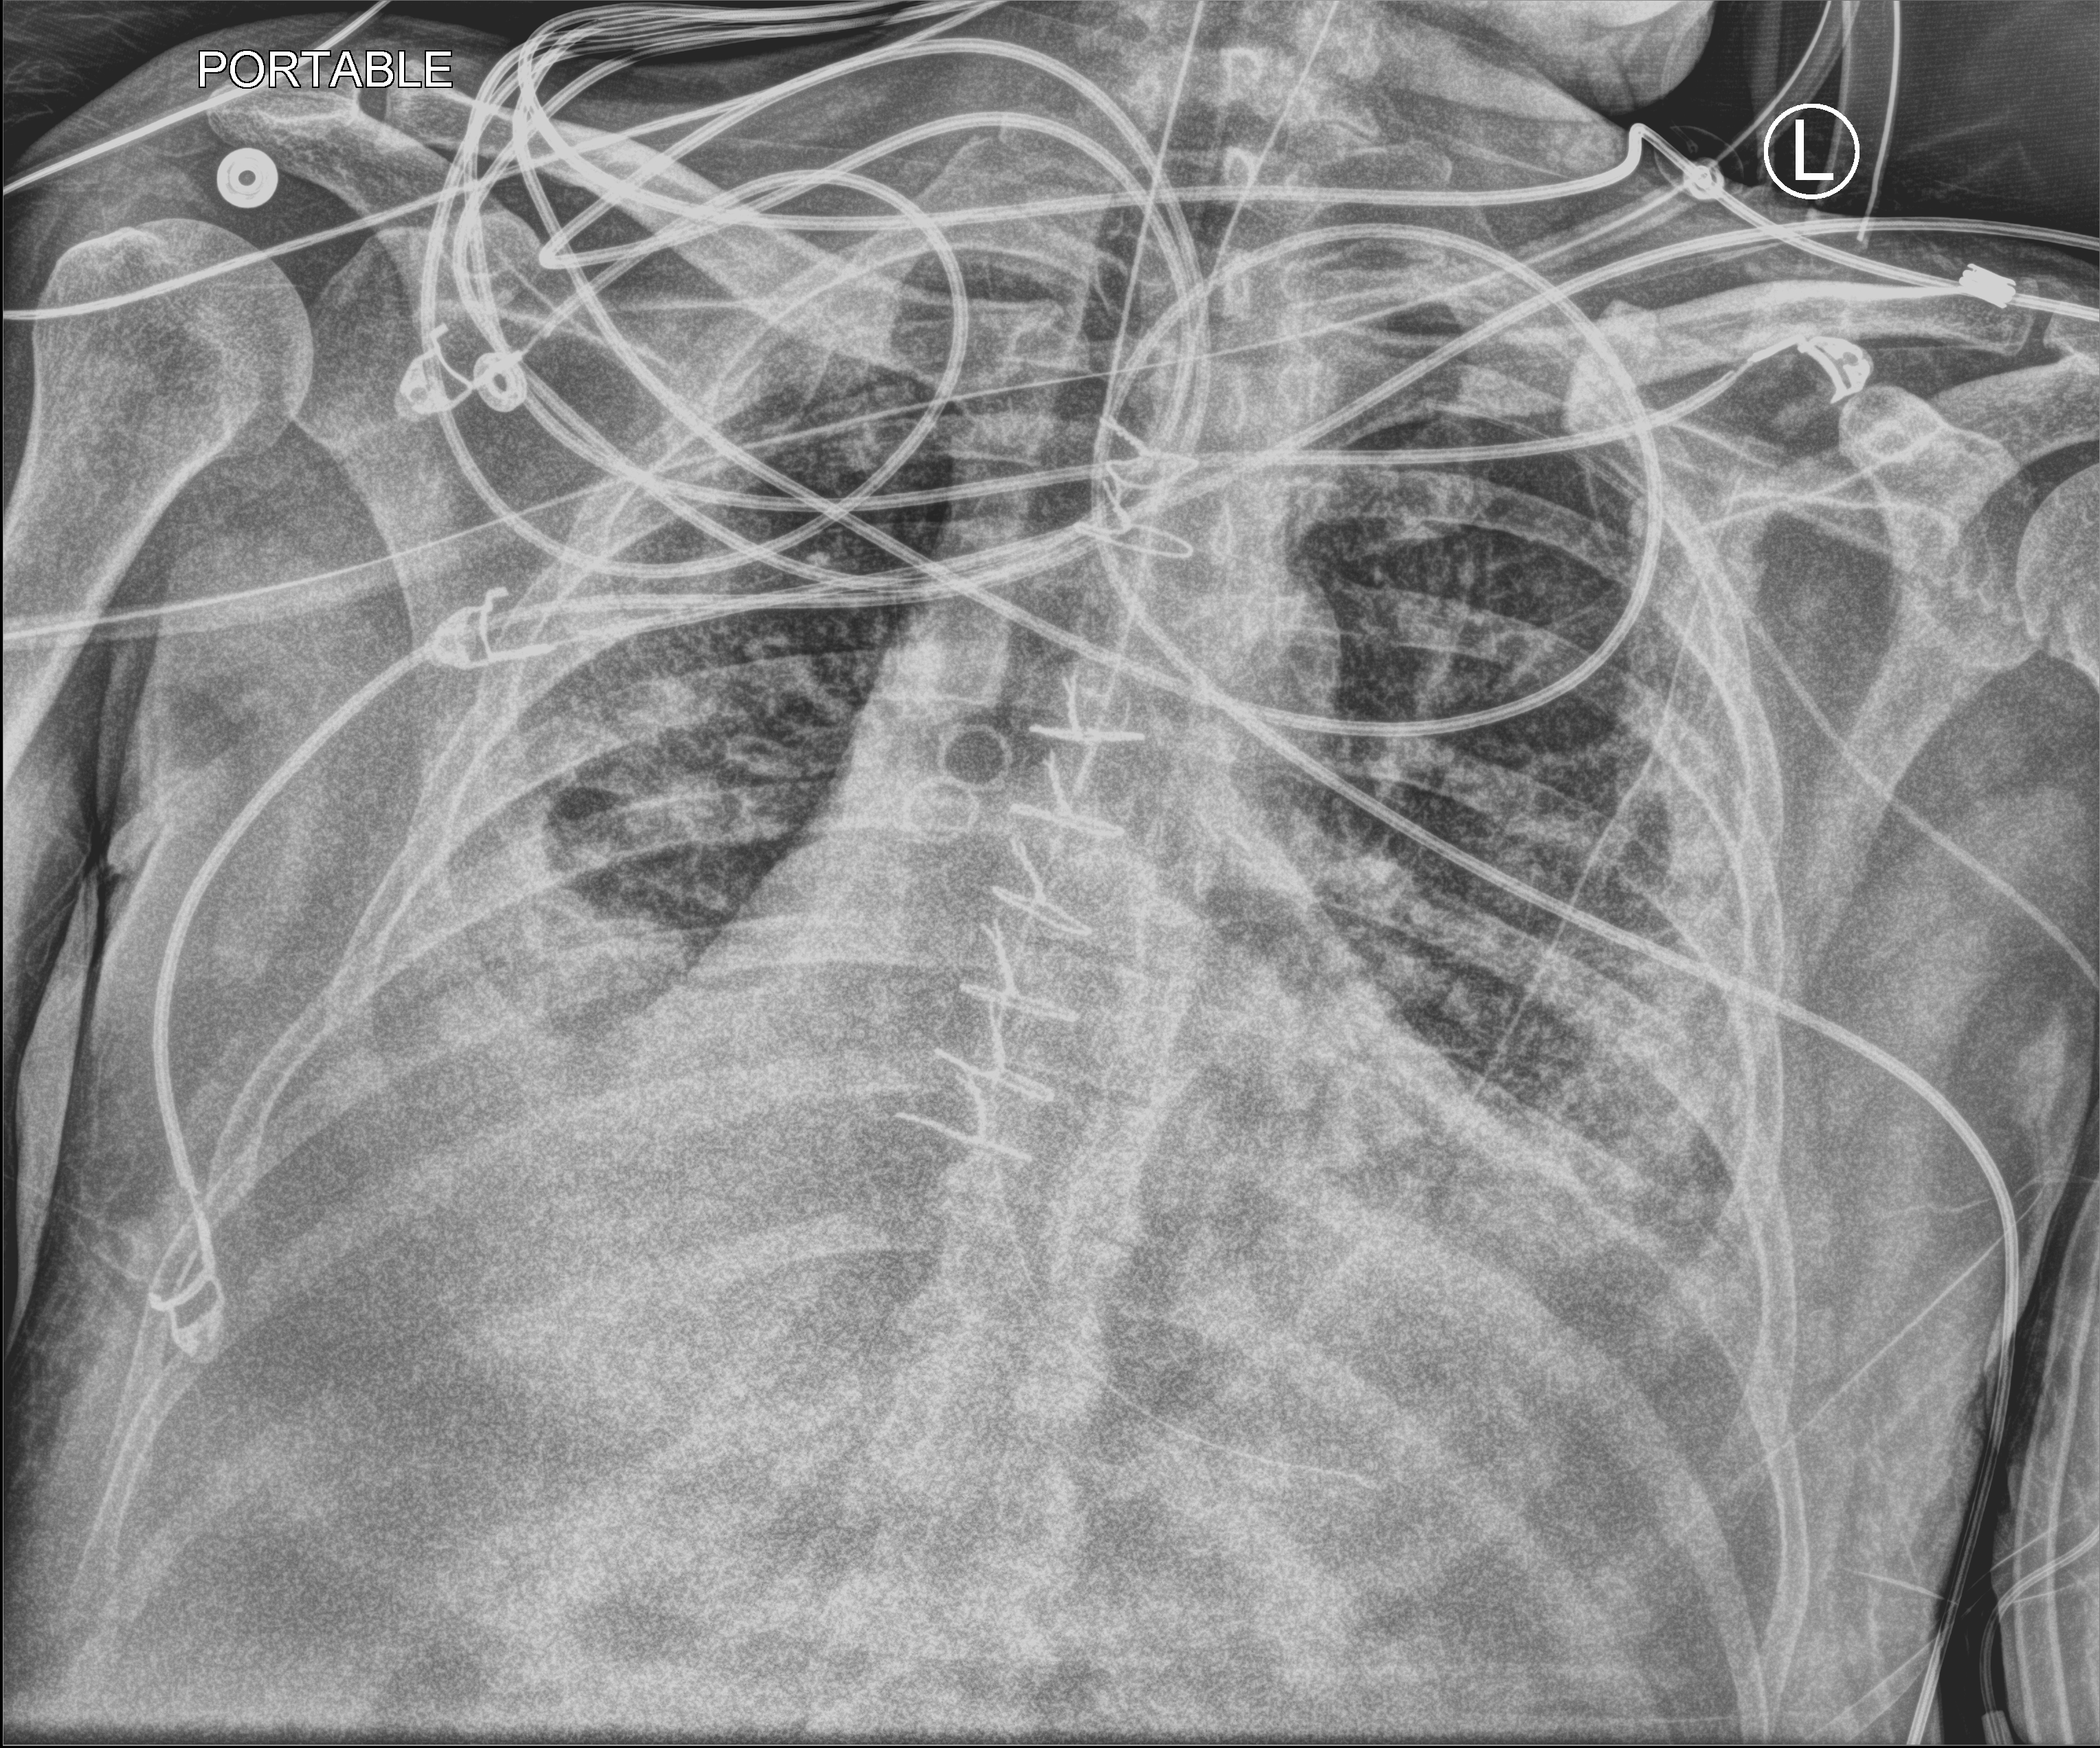
Portable chest radiograph; anteroposterior (AP) projection. Patient hospitalised with COVID-19; male, aged 18–59 years.
Admission-level facts for this patient (not findings on this image; timing relative to this image not recorded):
- chronic kidney disease (admission record): no
- admitted to intensive care during this hospital stay: yes